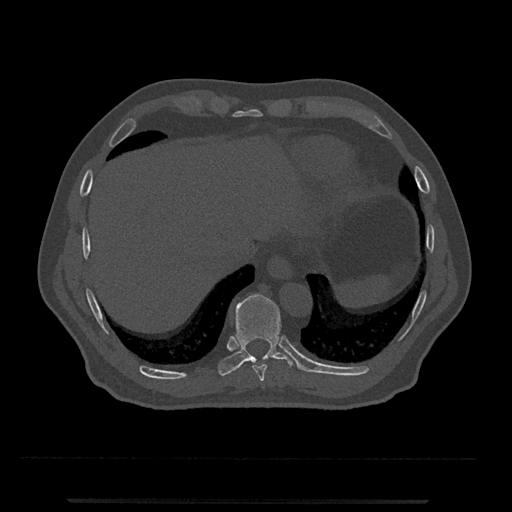
CT including the spine, one axial slice. Reconstruction kernel Br40s/3. Bone window (W 1800 / L 400 HU). 512 × 512 image matrix, field of view 419 × 419 mm. Male patient, age 63 years. From the clinical record (not read from this slice): primary cancer: prostate.
Annotated regions visible in this slice (semi-automatically segmented with operator editing):
- T10 vertebra: bounding box (x1, y1, x2, y2) in pixels: (218, 294, 299, 376)
- T9 vertebra: (252, 364, 267, 382)